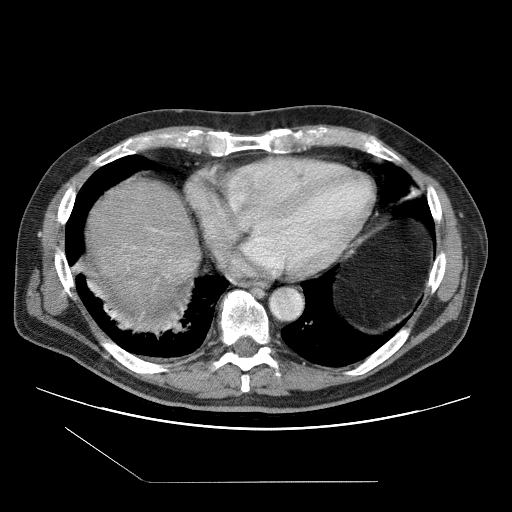
Contrast-enhanced abdominal CT (liver protocol), one axial slice; position 97 of 109 along the scan axis; 120 kVp; one of 2 acquisitions stored at this slice position; soft-tissue window (W 400 / L 40 HU); 2.5 mm slice thickness; 512 × 512 image matrix, field of view 400 × 400 mm. From the clinical record (not read from this slice): diagnosis: hepatocellular carcinoma (patient treated with transarterial chemoembolisation; whether this scan precedes or follows treatment is not stated here); TNM stage (as recorded): Stage-IIIB; Child-Pugh class: A; tumour differentiation: well differentiated; tumour nodularity: multinodular.
Annotated regions visible in this slice (semi-automatically segmented with operator editing):
- liver parenchyma outside the tumour (the mass and vessels are separate outlines, so this box may not span the whole liver): bounding box [x1, y1, x2, y2] px = [86, 180, 200, 315]